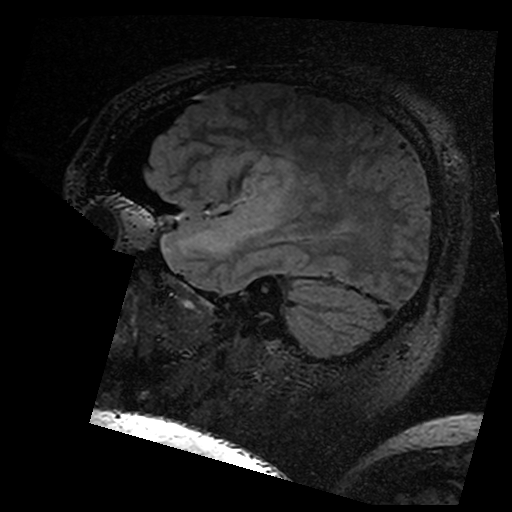
Brain MRI from a brain-tumour surgery series, one sagittal slice. Slice 126 of 176 in the series (ordered by position). T2 FLAIR. 1 mm slice thickness. 512 × 512 image matrix, field of view 250 × 250 mm. From the clinical record (not read from this slice): histopathology: Astrocytoma; WHO grade: 3; IDH mutation: yes.
Structures marked on this image (manually delineated by an expert):
- residual tumour: bounding box <219,155,294,199> (left, top, right, bottom; pixels)